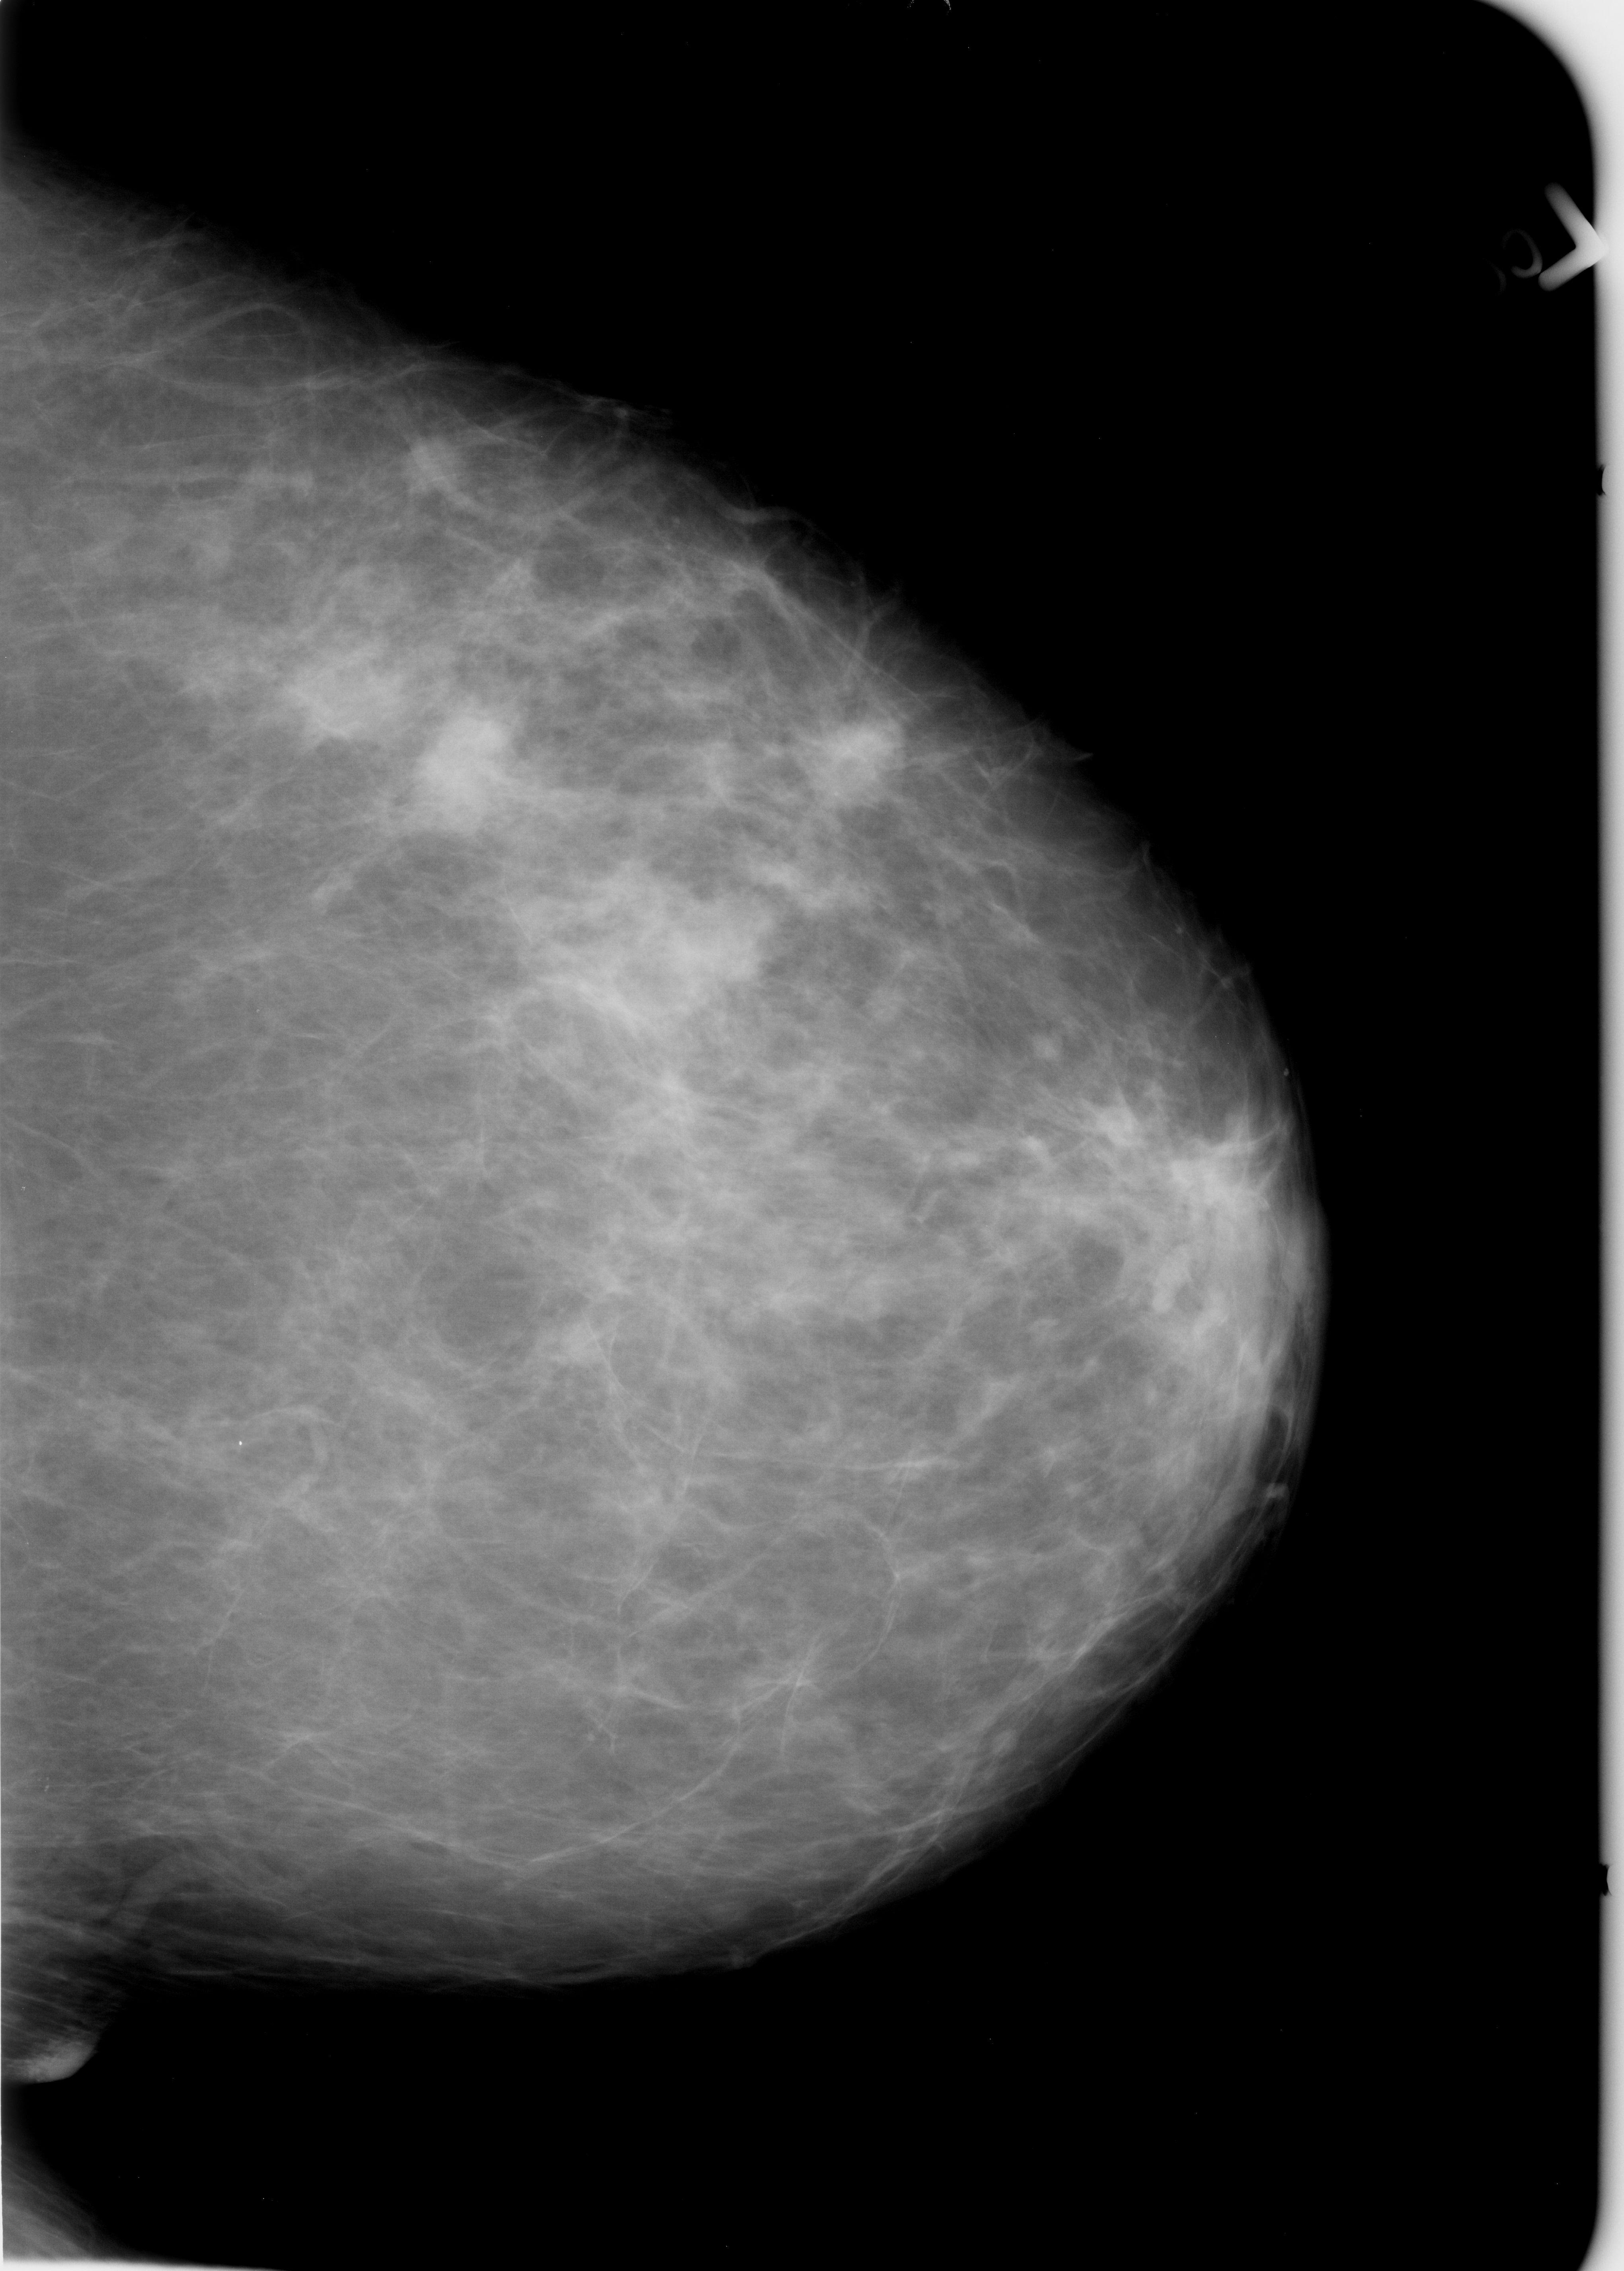
Digitized screen-film mammogram; left breast; craniocaudal (CC) view; 1624 × 2271 image matrix.
Expert-marked regions of interest on this film, with their recorded descriptors:
- Finding 1 of 3: mass, shape lobulated, margins circumscribed / ill defined; BI-RADS assessment category 3; pathology (as recorded): malignant: box from (x=409, y=711) to (x=519, y=823) px
- Finding 2 of 3: mass, shape lobulated, margins circumscribed / ill defined; BI-RADS assessment category 3; pathology result (as recorded, not read from the image): malignant: (x=655, y=902)–(x=770, y=1006)
- Finding 3 of 3: mass, shape lobulated, margins circumscribed / ill defined; BI-RADS assessment category 3; pathology (as recorded): malignant: (x=795, y=709)–(x=902, y=786)